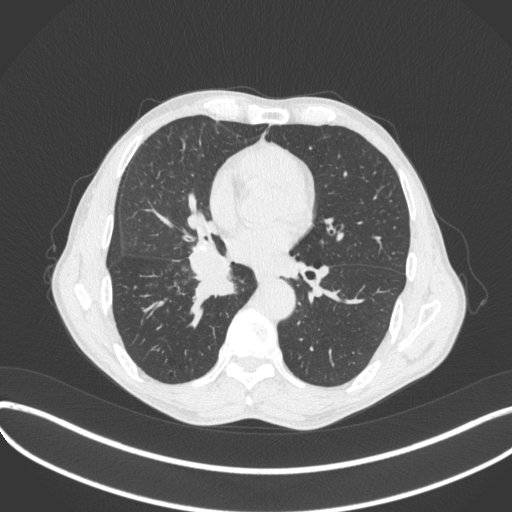
Chest CT, one axial slice. Position 207 of 481 along the scan axis. Reconstruction kernel B31f. Lung window (W 1500 / L -600 HU). 1 mm slice thickness. 512 × 512 image matrix, field of view 400 × 400 mm. Male patient, age 65 years. Case-level facts recorded for this patient, not image findings: clinical TNM (as recorded): T2a N0 M0; histopathological grade: G2.
Annotated regions visible in this slice (rectangle marked by the reading radiologist):
- lung tumour (recorded histology: squamous cell carcinoma): bounding box [x1, y1, x2, y2] px = [183, 238, 244, 305]